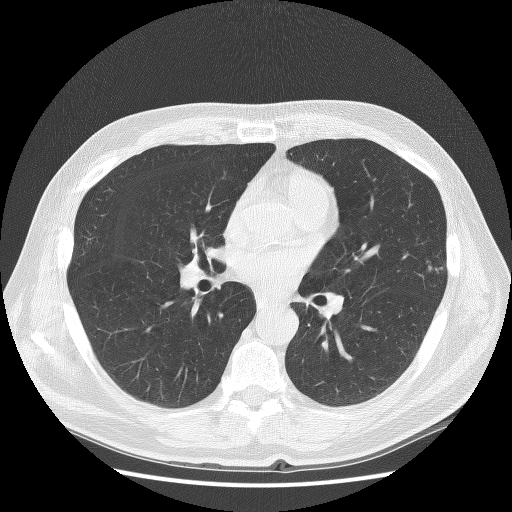
Axial slice from a low-dose chest CT screening exam. First (baseline) screen. Lung window (W 1500 / L -600 HU). 120 kVp. Male, age 67 years at enrolment. Former smoker at enrolment.
• Expert-annotated lung lesion, bounding box [x1, y1, x2, y2] px = [405, 246, 463, 294].
• No non-calcified nodule or mass ≥4 mm was recorded by the screening reader at this exam.
• Official screen result: negative screen, minor abnormalities not suspicious for lung cancer.
• Later outcome: lung cancer diagnosed 772 days after this screen — squamous cell carcinoma, NOS, left upper lobe, moderately differentiated (G2), stage IB (AJCC 6th edition), 25 mm at pathology.